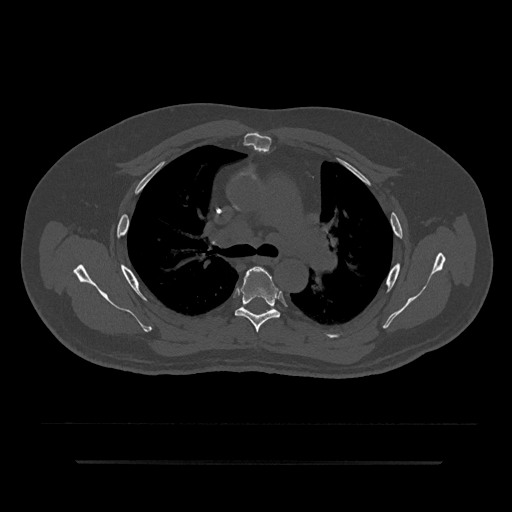
CT including the spine, one axial slice. Position 574 of 797 along the scan axis. Reconstruction kernel Br40s/3. Bone window (W 1800 / L 400 HU). 0.5 mm slice thickness. 512 × 512 image matrix, field of view 464 × 464 mm. Patient: male, 59 years. Case-level facts recorded for this patient, not image findings: primary cancer: bile ducts.
Structures marked on this image (semi-automatically segmented with operator editing):
- T5 vertebra: bounding box (x1, y1, x2, y2) in pixels: (234, 266, 280, 333)